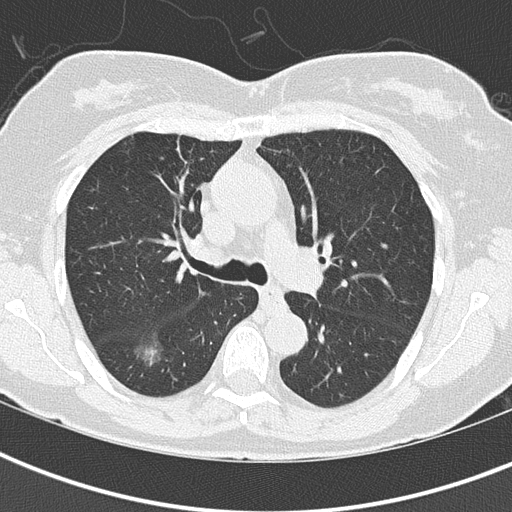
Axial slice from a low-dose chest CT screening exam; baseline screening round; lung window (W 1500 / L -600 HU); lung (sharp) reconstruction kernel (B50f). Female, age 68 years at enrolment.
- Expert reader's lesion annotation, box from (x=119, y=326) to (x=178, y=378) px.
- Screening reader's record for this exam (one nodule recorded; not confirmed to be the boxed lesion): non-calcified nodule or mass ≥4 mm, right lower lobe, 19 × 17 mm, spiculated (stellate) margins, ground glass attenuation.
- Later outcome: lung cancer diagnosed 40 days after this screen — bronchiolo-alveolar adenocarcinoma, NOS, right lower lobe, well differentiated (G1), stage IA (AJCC 6th edition), 15 mm at pathology.